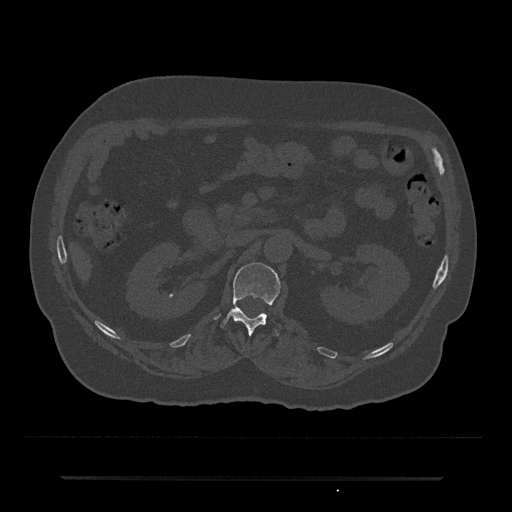
CT including the spine, one axial slice; 120 kVp; bone window (W 1800 / L 400 HU); 512 × 512 image matrix, field of view 437 × 437 mm. Patient: male, 69 years. From the clinical record (not read from this slice): primary cancer: prostate.
Annotated regions visible in this slice (semi-automatic segmentation, software-assisted and operator-edited):
- L1 vertebra: box from (x=221, y=262) to (x=280, y=335) px